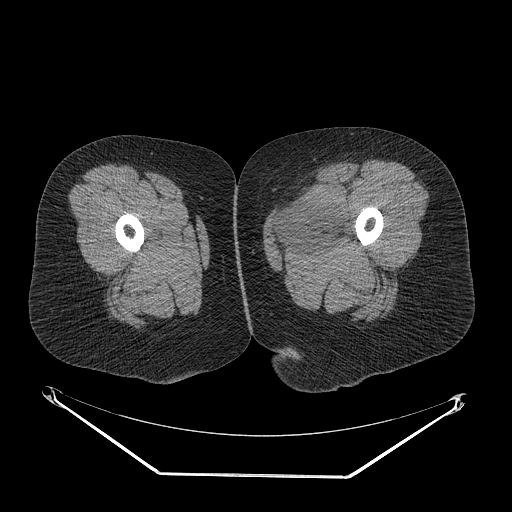
CT of an extremity soft-tissue mass (from a PET/CT study), one axial slice. Position 17 of 267 along the scan axis. 140 kVp. Soft-tissue window (W 400 / L 40 HU). 512 × 512 image matrix, field of view 500 × 500 mm. Female patient. From the clinical record (not read from this slice): histological type: myxofibrosarcoma; grade: intermediate; site of the primary tumour: left thigh.
Structures marked on this image (expert contour drawn on MRI and transferred to this co-registered scan by the dataset authors):
- gross tumour volume including surrounding oedema: box from (x=274, y=196) to (x=350, y=248) px
- gross tumour volume (mass): (x=281, y=196)–(x=344, y=247)